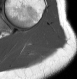
MRI of an extremity soft-tissue mass, one axial slice. Slice 21 of 28 in the series (ordered by position). MR volume resampled by the dataset authors to the PET/CT grid (not the native acquisition matrix). 3.27 mm slice thickness. 77 × 79 image matrix, field of view 75 × 77 mm. Female patient. Case-level facts recorded for this patient, not image findings: histological type: malignant fibrous histiocytoma; grade: low; site of the primary tumour: left arm.
Outlined on this slice (expert contour drawn on MRI and transferred to this co-registered scan by the dataset authors):
- gross tumour volume (mass): bounding box <24,48,36,55> (left, top, right, bottom; pixels)